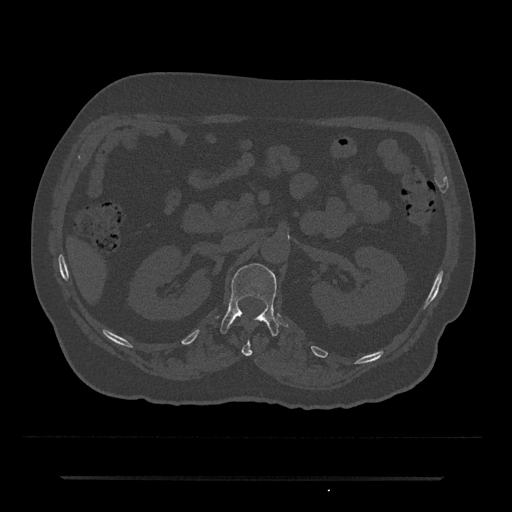
CT including the spine, one axial slice. Position 84 of 797 along the scan axis. Bone window (W 1800 / L 400 HU). 0.5 mm slice thickness. 512 × 512 image matrix. Male patient, age 69 years. From the clinical record (not read from this slice): primary cancer: prostate.
Annotated regions visible in this slice (semi-automatic segmentation, software-assisted and operator-edited):
- L1 vertebra: bounding box (x1, y1, x2, y2) in pixels: (220, 263, 279, 336)
- T12 vertebra: (242, 340, 252, 356)